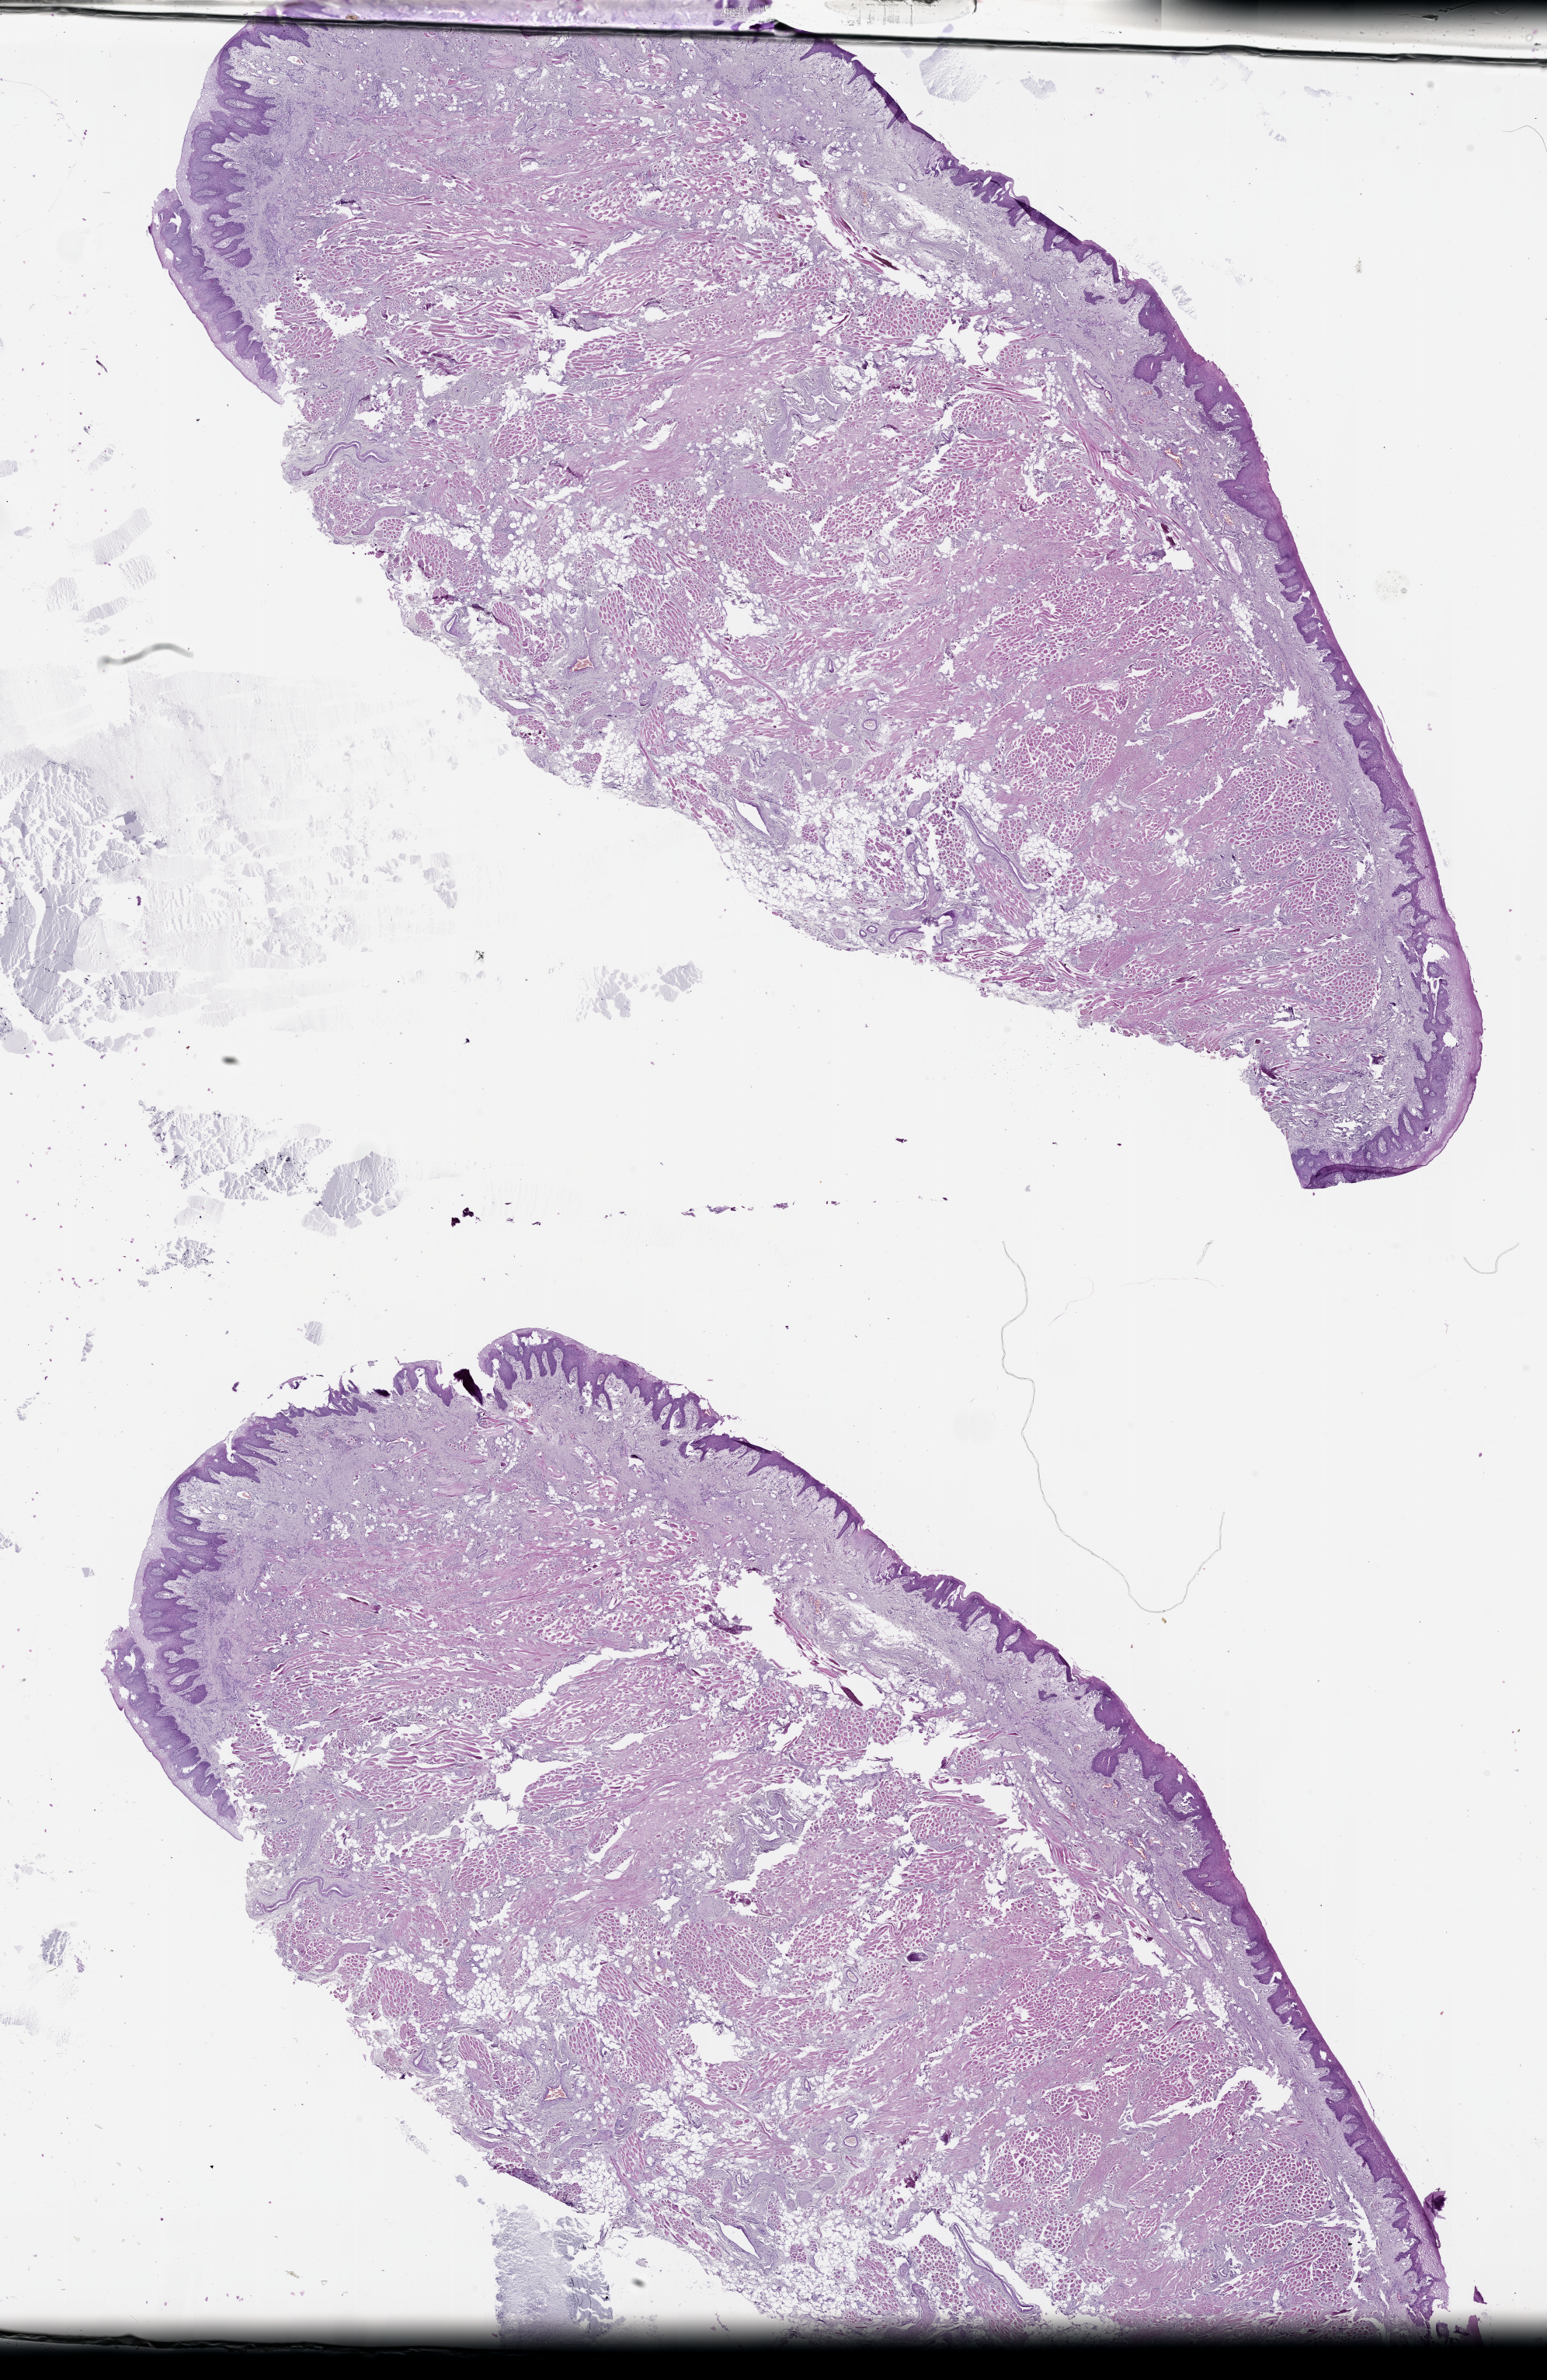
Whole-slide histology image, H&E-stained, whole scanned area (about 16.0 x 24.7 mm) shown as a low-resolution overview, head and neck, tissue type not recorded.
• patient diagnosis (cohort enrolment): head and neck cancer (head-neck)